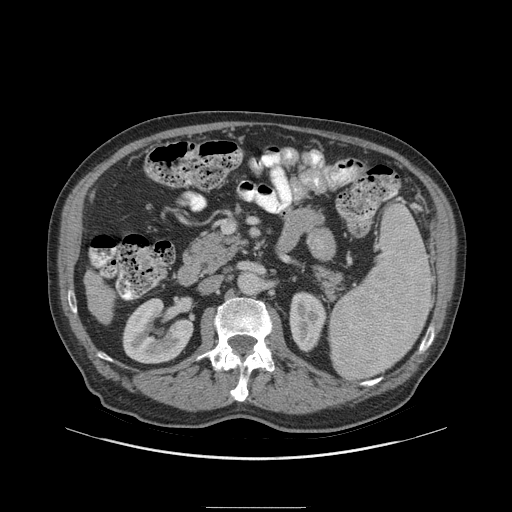
Contrast-enhanced abdominal CT (liver protocol), one axial slice. Slice 29 of 105 in the series (ordered by position). Reconstruction kernel STANDARD. 140 kVp. Soft-tissue window (W 400 / L 40 HU). 512 × 512 image matrix, field of view 440 × 440 mm. Case-level facts recorded for this patient, not image findings: diagnosis: hepatocellular carcinoma (patient treated with transarterial chemoembolisation; whether this scan precedes or follows treatment is not stated here); TNM stage (as recorded): Stage-I; Child-Pugh class: A; tumour nodularity: uninodular.
Outlined on this slice (semi-automatically segmented with operator editing):
- liver parenchyma outside the tumour (the mass and vessels are separate outlines, so this box may not span the whole liver): bounding box [x1, y1, x2, y2] px = [84, 270, 114, 324]